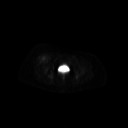
FDG PET of an extremity soft-tissue mass (from a PET/CT study), one axial slice. Position 66 of 267 along the scan axis. 128 × 128 image matrix, field of view 700 × 700 mm. Patient: female, 56 years. Case-level facts recorded for this patient, not image findings: histological type: malignant solitary fibrous tumor; grade: intermediate; site of the primary tumour: right thigh.
Structures marked on this image (expert contour drawn on MRI and transferred to this co-registered scan by the dataset authors):
- gross tumour volume including surrounding oedema: box from (x=37, y=54) to (x=49, y=62) px